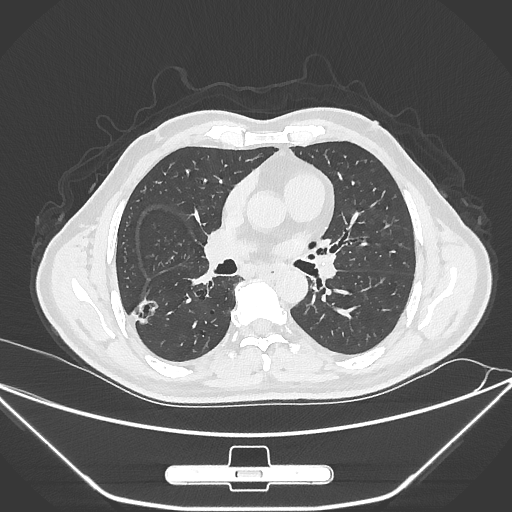
Chest CT, one axial slice. Slice 154 of 310 in the series (ordered by position). 120 kVp. Lung window (W 1500 / L -600 HU). 1 mm slice thickness. 512 × 512 image matrix, field of view 398 × 398 mm. Male patient, age 71 years. From the clinical record (not read from this slice): clinical TNM (as recorded): T1c N0 M0; histopathological grade: G2.
Outlined on this slice (bounding box drawn by a radiologist):
- lung tumour (recorded histology: adenocarcinoma): bounding box (x1, y1, x2, y2) in pixels: (127, 287, 169, 336)